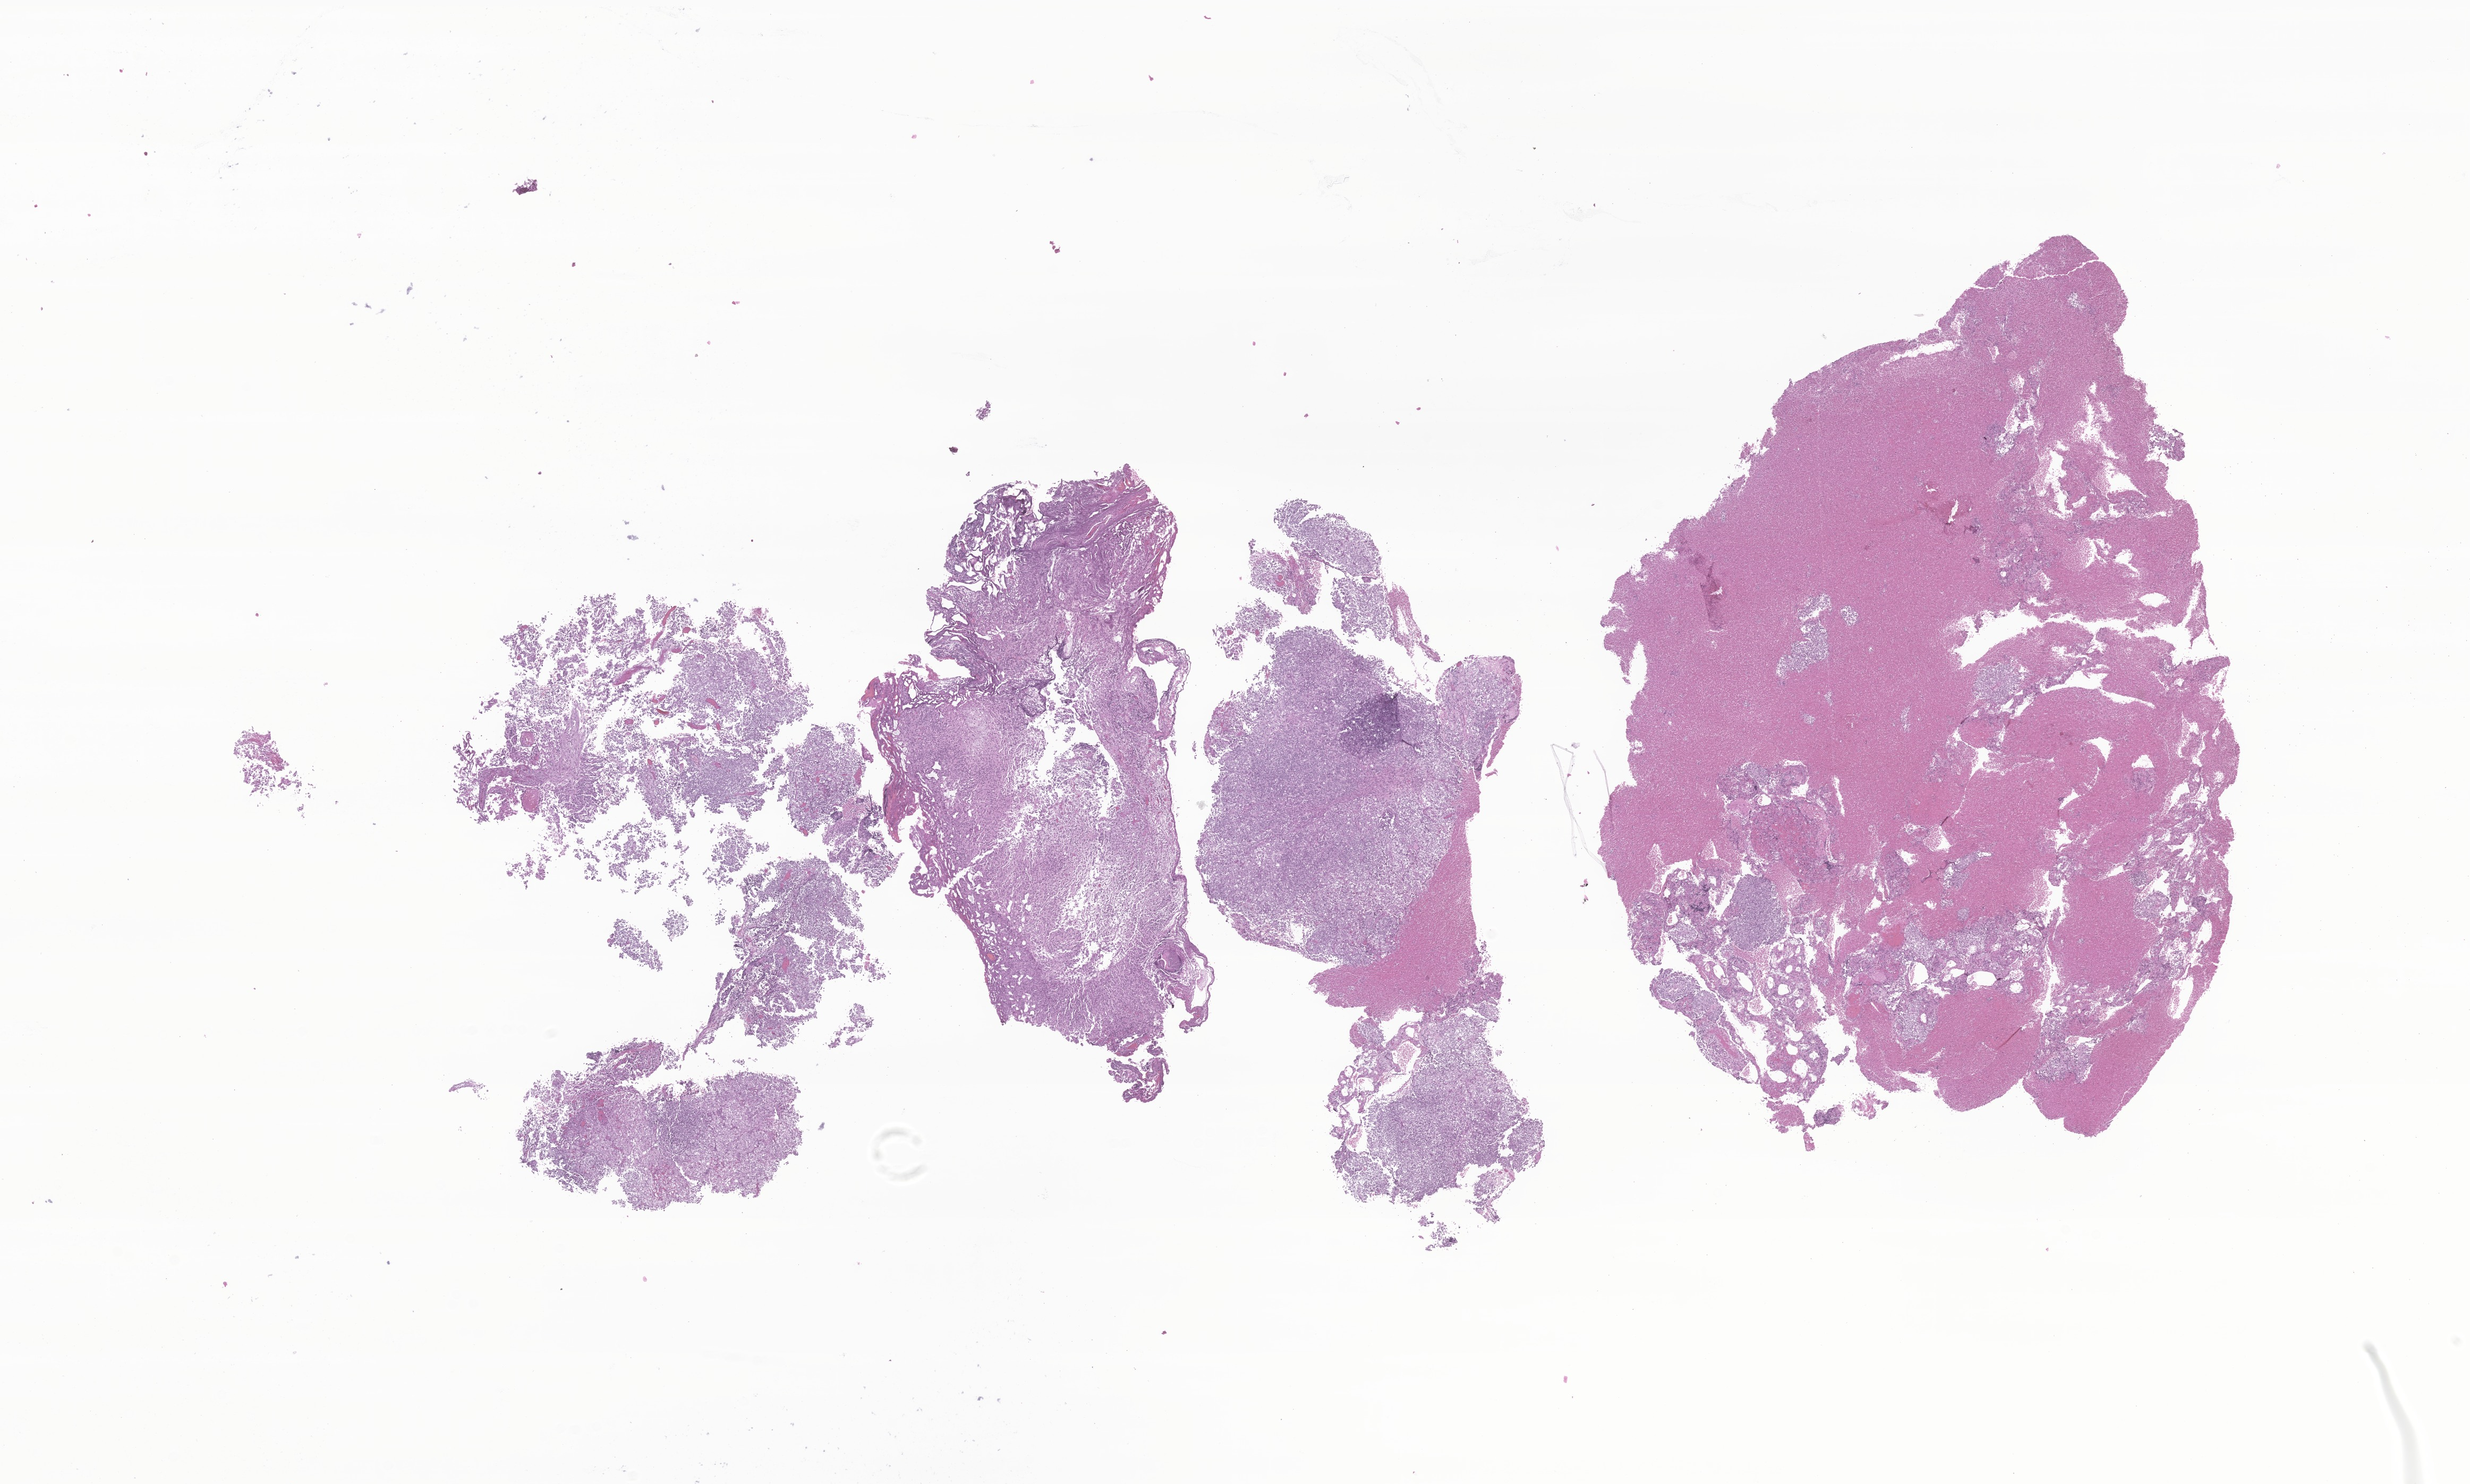
Whole-slide image, H&E stain of tumor tissue from the cerebellum — low-resolution overview of the scanned area, about 19.6 x 11.8 mm. Formalin-fixed paraffin-embedded section. Patient: male, age 336 days.
• recorded diagnosis: Atypical teratoid/rhabdoid tumor